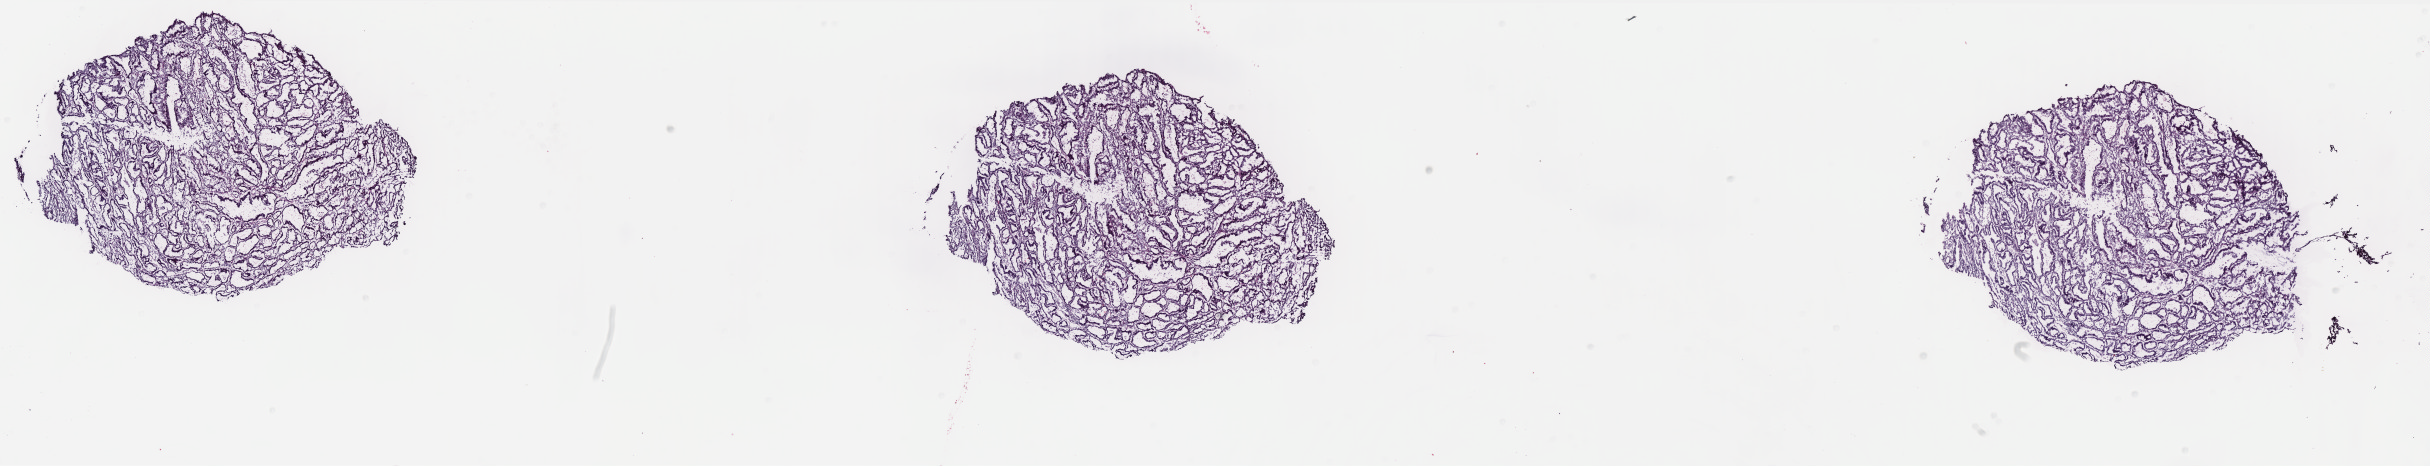
H&E-stained whole-slide image — shown as a low-resolution overview of the whole scanned area (about 39.0 x 7.5 mm). Frozen section from the bottom of the tissue portion. Uterus, primary tumour sample. Patient: female, age at initial diagnosis 75 years. Histologic grade: G2 (moderately differentiated). Slide review estimates, as recorded: tumour cells 100%, tumour nuclei 85%, normal cells 0%, stromal cells 0%, necrosis 0%. Infiltration values recorded for this section: lymphocyte infiltration 0%, monocyte infiltration 0%, neutrophil infiltration 0%.
FIGO stage: IA. Pathologic diagnosis: Endometrioid adenocarcinoma, NOS (endometrium). Lymph nodes positive (case pathology): 0 of 3 examined.